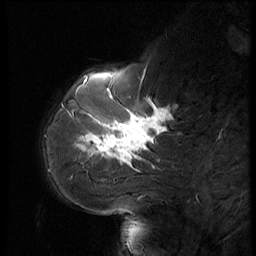
Breast MRI (dynamic contrast-enhanced), one sagittal slice; slice 17 of 56 in the series (ordered by position); dynamic contrast-enhanced series, image 2 of 3 at this slice position (ordered by acquisition); 1.5 T; TE 4.2 ms, TR 9 ms; 2.5 mm slice thickness; 256 × 256 image matrix. Patient: female, 61 years. From the clinical record (not read from this slice): setting: breast cancer imaged before/during neoadjuvant chemotherapy; receptor status: HR-positive, HER2-negative.
Outlined on this slice (semi-automatic segmentation, software-assisted and operator-edited):
- analysis volume of interest (the breast-tissue region the enhancement analysis was run in; not a lesion): bounding box <65,74,185,175> (left, top, right, bottom; pixels)
- tumour enhancement mask (voxels above the 140 % enhancement threshold inside the analysis volume of interest): <79,93,172,167>